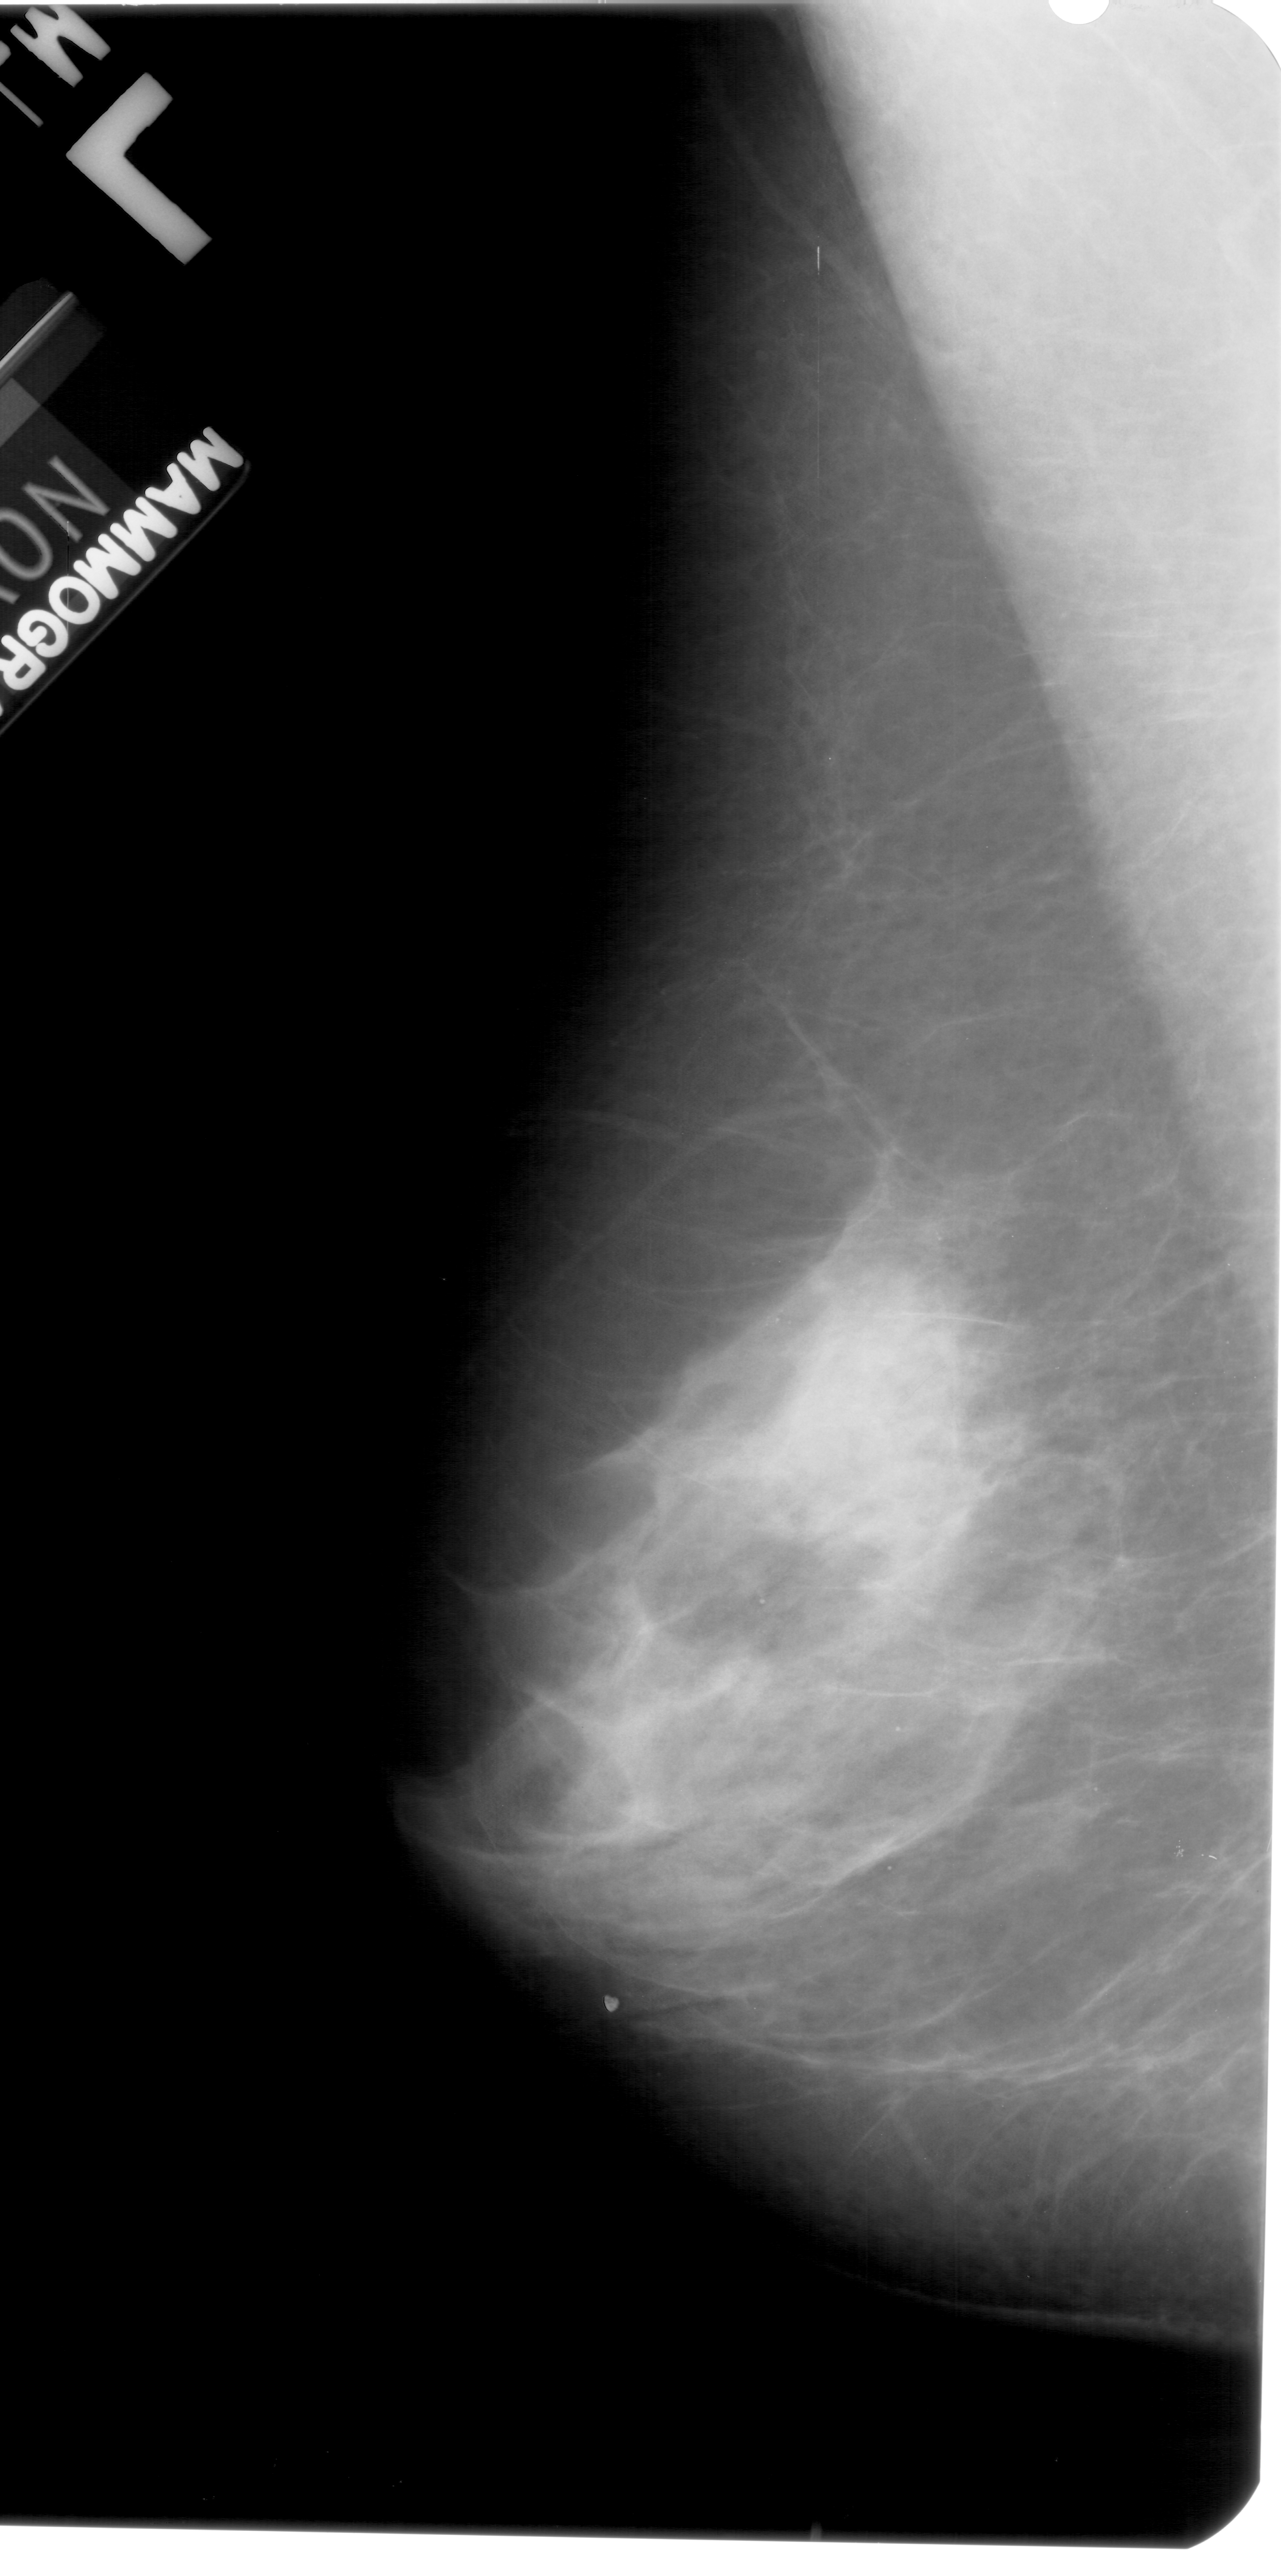
Scanned film-screen mammogram, left breast, mediolateral oblique (MLO) view, breast composition: extremely dense (BI-RADS density category 4 of 4).
Radiologist-marked abnormalities on this image: calcifications, morphology pleomorphic, distribution clustered; BI-RADS assessment category 4; pathology result (as recorded, not read from the image): benign.